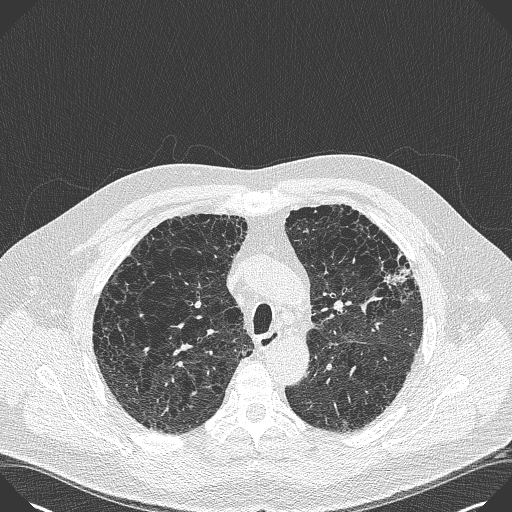
Chest CT (low-dose screening protocol), one axial image; baseline screening round; lung window (W 1500 / L -600 HU); 1 mm slice thickness; slice 118 of 383 in the series; 512 × 512 image matrix, field of view 380 × 380 mm. Male participant, aged 59 years at enrolment. Current smoker at enrolment.
Expert-annotated lung lesion, bounding box (x1, y1, x2, y2) in pixels: (374, 243, 427, 294). No non-calcified nodule or mass ≥4 mm was recorded by the screening reader at this exam. Participant outcome: lung cancer diagnosed 909 days after this screen (after the third annual screen) — bronchiolo-alveolar carcinoma, mixed mucinous and non-mucinous, left upper lobe, stage IA (AJCC 6th edition), 20 mm at pathology.